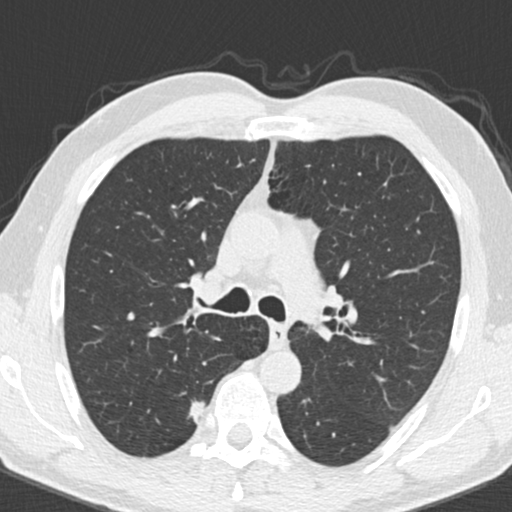
Low-dose screening chest CT, one axial slice. Reconstruction kernel B30f. 120 kVp. Lung window (W 1500 / L -600 HU). 512 × 512 image matrix, field of view 307 × 307 mm.
Annotated regions visible in this slice (manually delineated by an expert):
- lesion 1 (tumor, upper lobe of right lung): bounding box <187,400,207,423> (left, top, right, bottom; pixels)